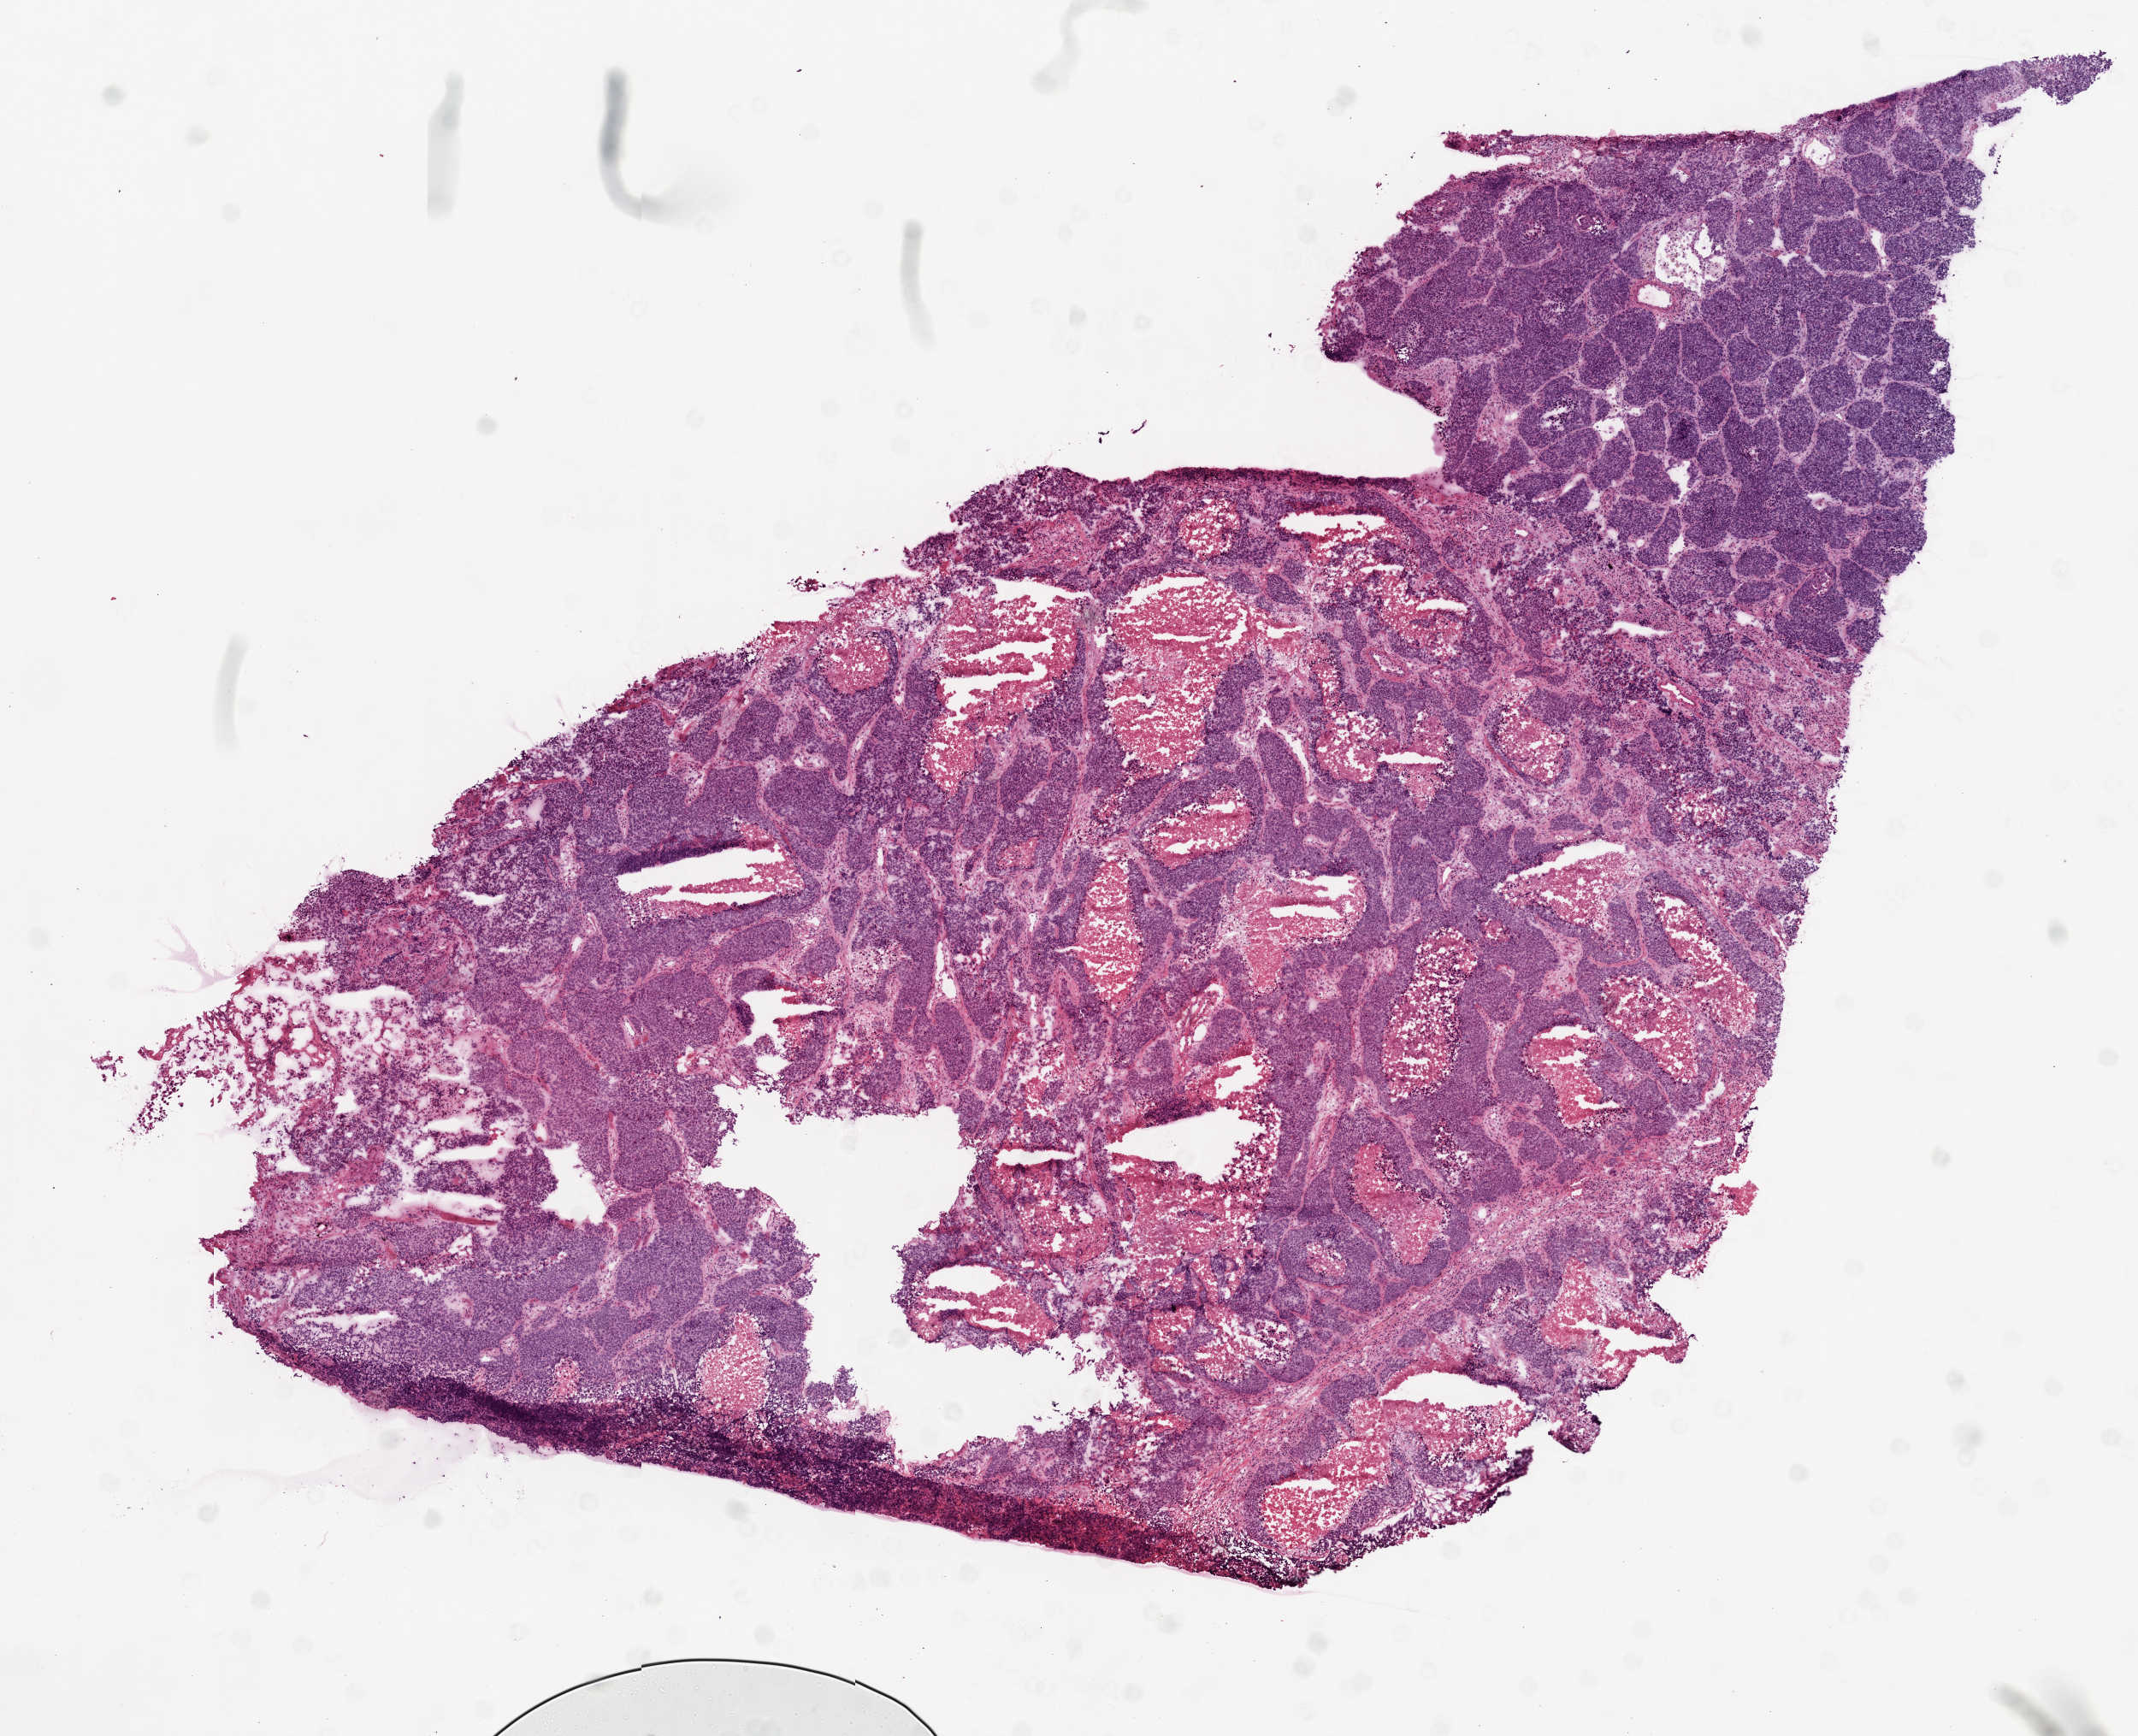
H&E-stained whole-slide image — low-resolution overview of the scanned area, about 10.0 x 8.1 mm, frozen section from the top of the tissue portion, primary tumour sample from the lung. Female, age 63 years at initial diagnosis. Pathologist review of this section (percent, as recorded): tumour cells 65%, tumour nuclei 80%, normal cells 0%, stromal cells 10%, necrosis 25%.
Diagnosis: Squamous cell carcinoma, small cell, nonkeratinizing (middle lobe, lung). AJCC pathologic stage: IB (6th edition).